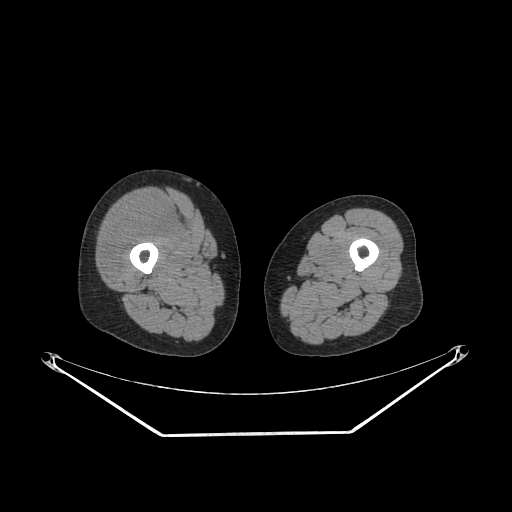
CT of an extremity soft-tissue mass (from a PET/CT study), one axial slice. Slice 230 of 311 in the series (ordered by position). 140 kVp. Soft-tissue window (W 400 / L 40 HU). 512 × 512 image matrix, field of view 500 × 500 mm. Female patient. From the clinical record (not read from this slice): histological type: pleiomorphic undifferentiated sarcoma; grade: high; site of the primary tumour: right quadricep.
Annotated regions visible in this slice (expert contour drawn on MRI and transferred to this co-registered scan by the dataset authors):
- tumour plus oedema (research contour): bounding box (x1, y1, x2, y2) in pixels: (103, 203, 181, 277)